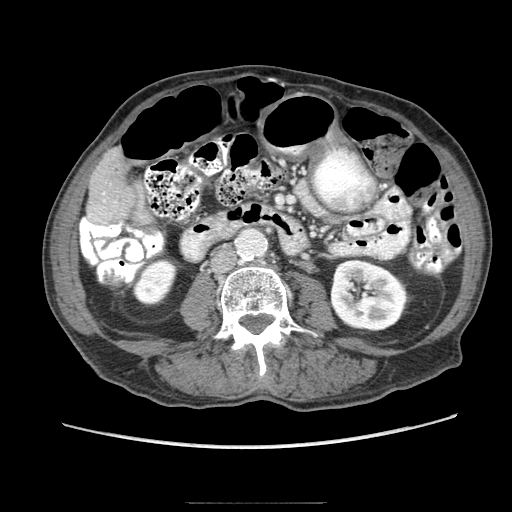
Contrast-enhanced abdominal CT (liver protocol), one axial slice. Position 15 of 83 along the scan axis. Reconstruction kernel STANDARD. Soft-tissue window (W 400 / L 40 HU). 2.5 mm slice thickness. 512 × 512 image matrix, field of view 360 × 360 mm. From the clinical record (not read from this slice): diagnosis: hepatocellular carcinoma (patient treated with transarterial chemoembolisation; whether this scan precedes or follows treatment is not stated here); TNM stage (as recorded): Stage-I; Child-Pugh class: A; tumour differentiation: moderately differentiated; tumour nodularity: uninodular.
Annotated regions visible in this slice (semi-automatic segmentation, software-assisted and operator-edited):
- liver parenchyma outside the tumour (the mass and vessels are separate outlines, so this box may not span the whole liver): box from (x=86, y=148) to (x=136, y=224) px
- liver vessels: (x=89, y=193)–(x=106, y=222)